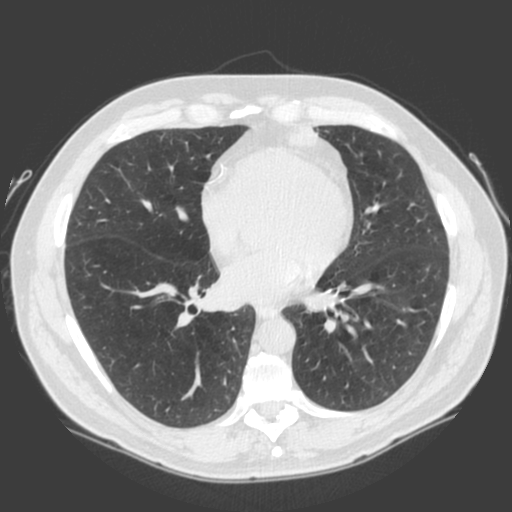
Low-dose screening chest CT, one axial slice. Slice 83 of 185 in the series (ordered by position). Lung window (W 1500 / L -600 HU). 2 mm slice thickness. 512 × 512 image matrix.
Structures marked on this image (manually delineated by an expert):
- lesion 1 (tumor, lower lobe of left lung): bounding box [x1, y1, x2, y2] px = [287, 121, 320, 147]